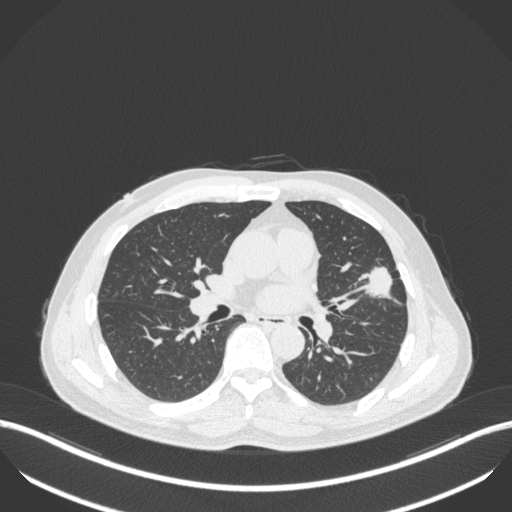
Chest CT, one axial slice. Lung window (W 1500 / L -600 HU). 512 × 512 image matrix, field of view 400 × 400 mm. Patient: male, 55 years. Case-level facts recorded for this patient, not image findings: clinical TNM (as recorded): T1c N0 M0.
Annotated regions visible in this slice (rectangle marked by the reading radiologist):
- lung tumour (recorded histology: adenocarcinoma): box from (x=361, y=264) to (x=405, y=311) px